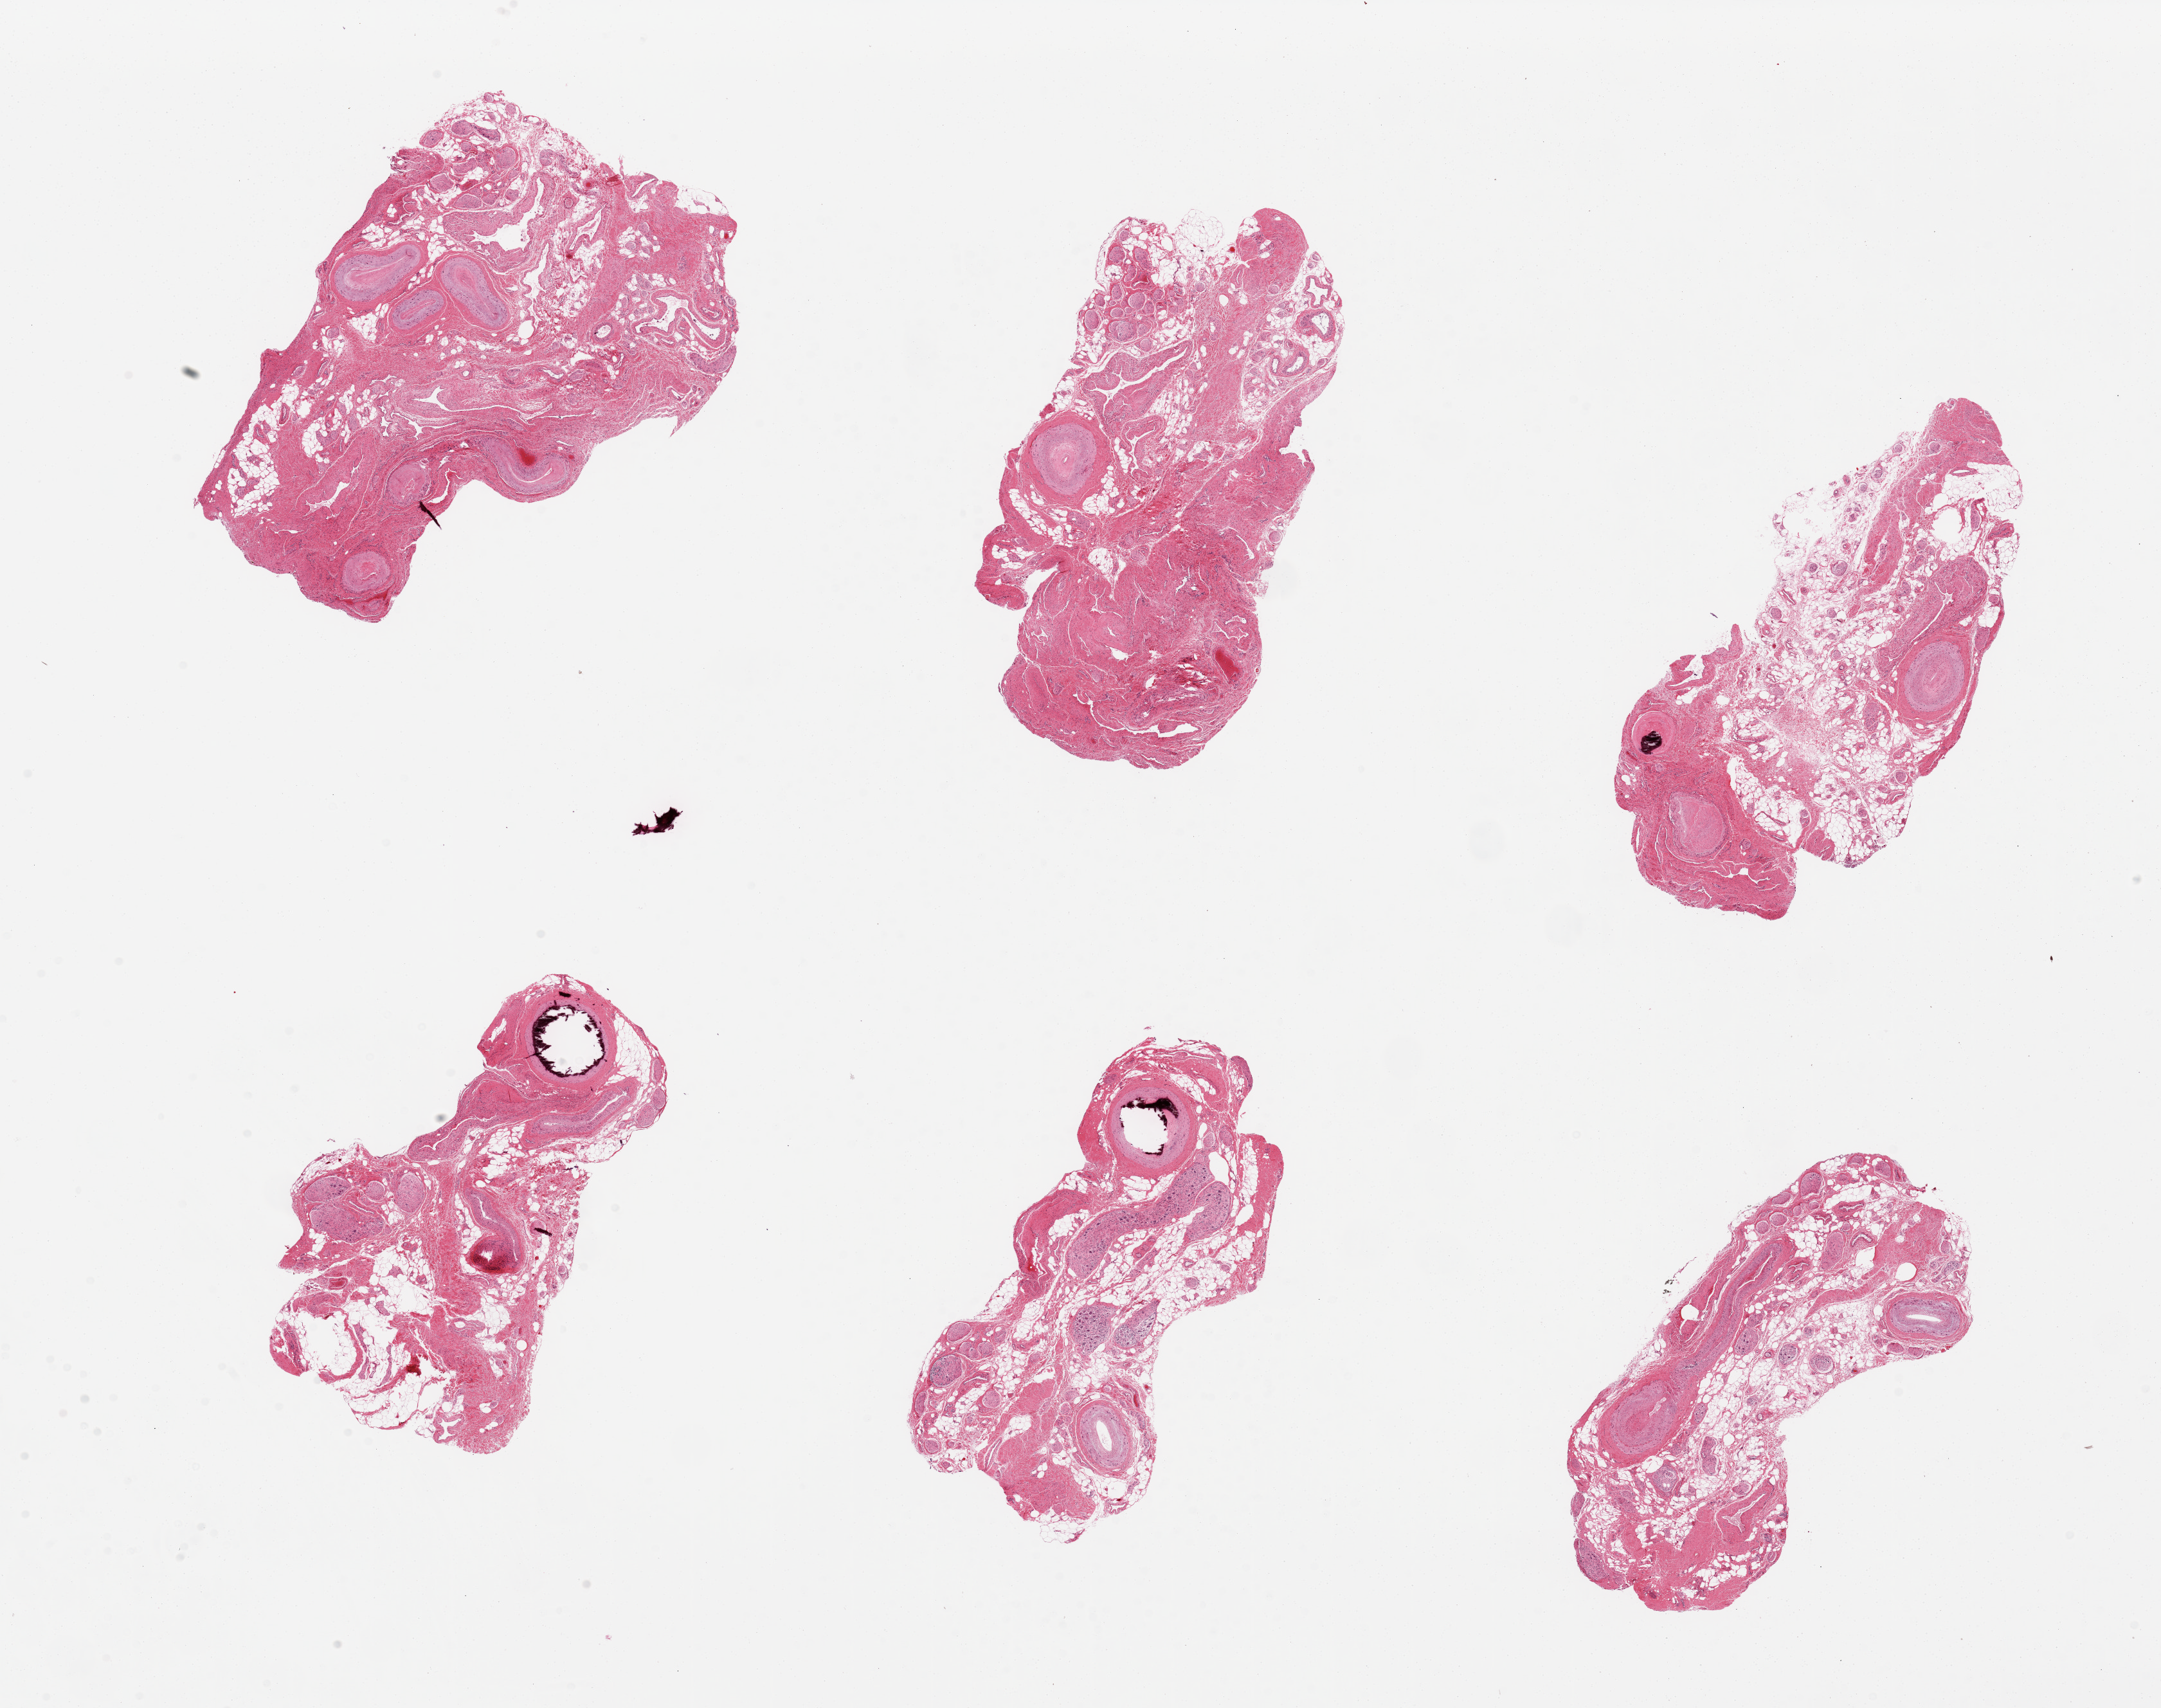
Digitized haematoxylin and eosin-stained section — low-resolution overview of the scanned area, about 26.6 x 21.0 mm (from a 20x scan), PAXgene-fixed paraffin-embedded (PFPE) section, section of vagina (target tissue), tissue donor sample. Female donor.
Pathologist's review note for this sample: 6 pieces fibrovascular and adipose tissue, unknown provenance; not vaginal mucosa.